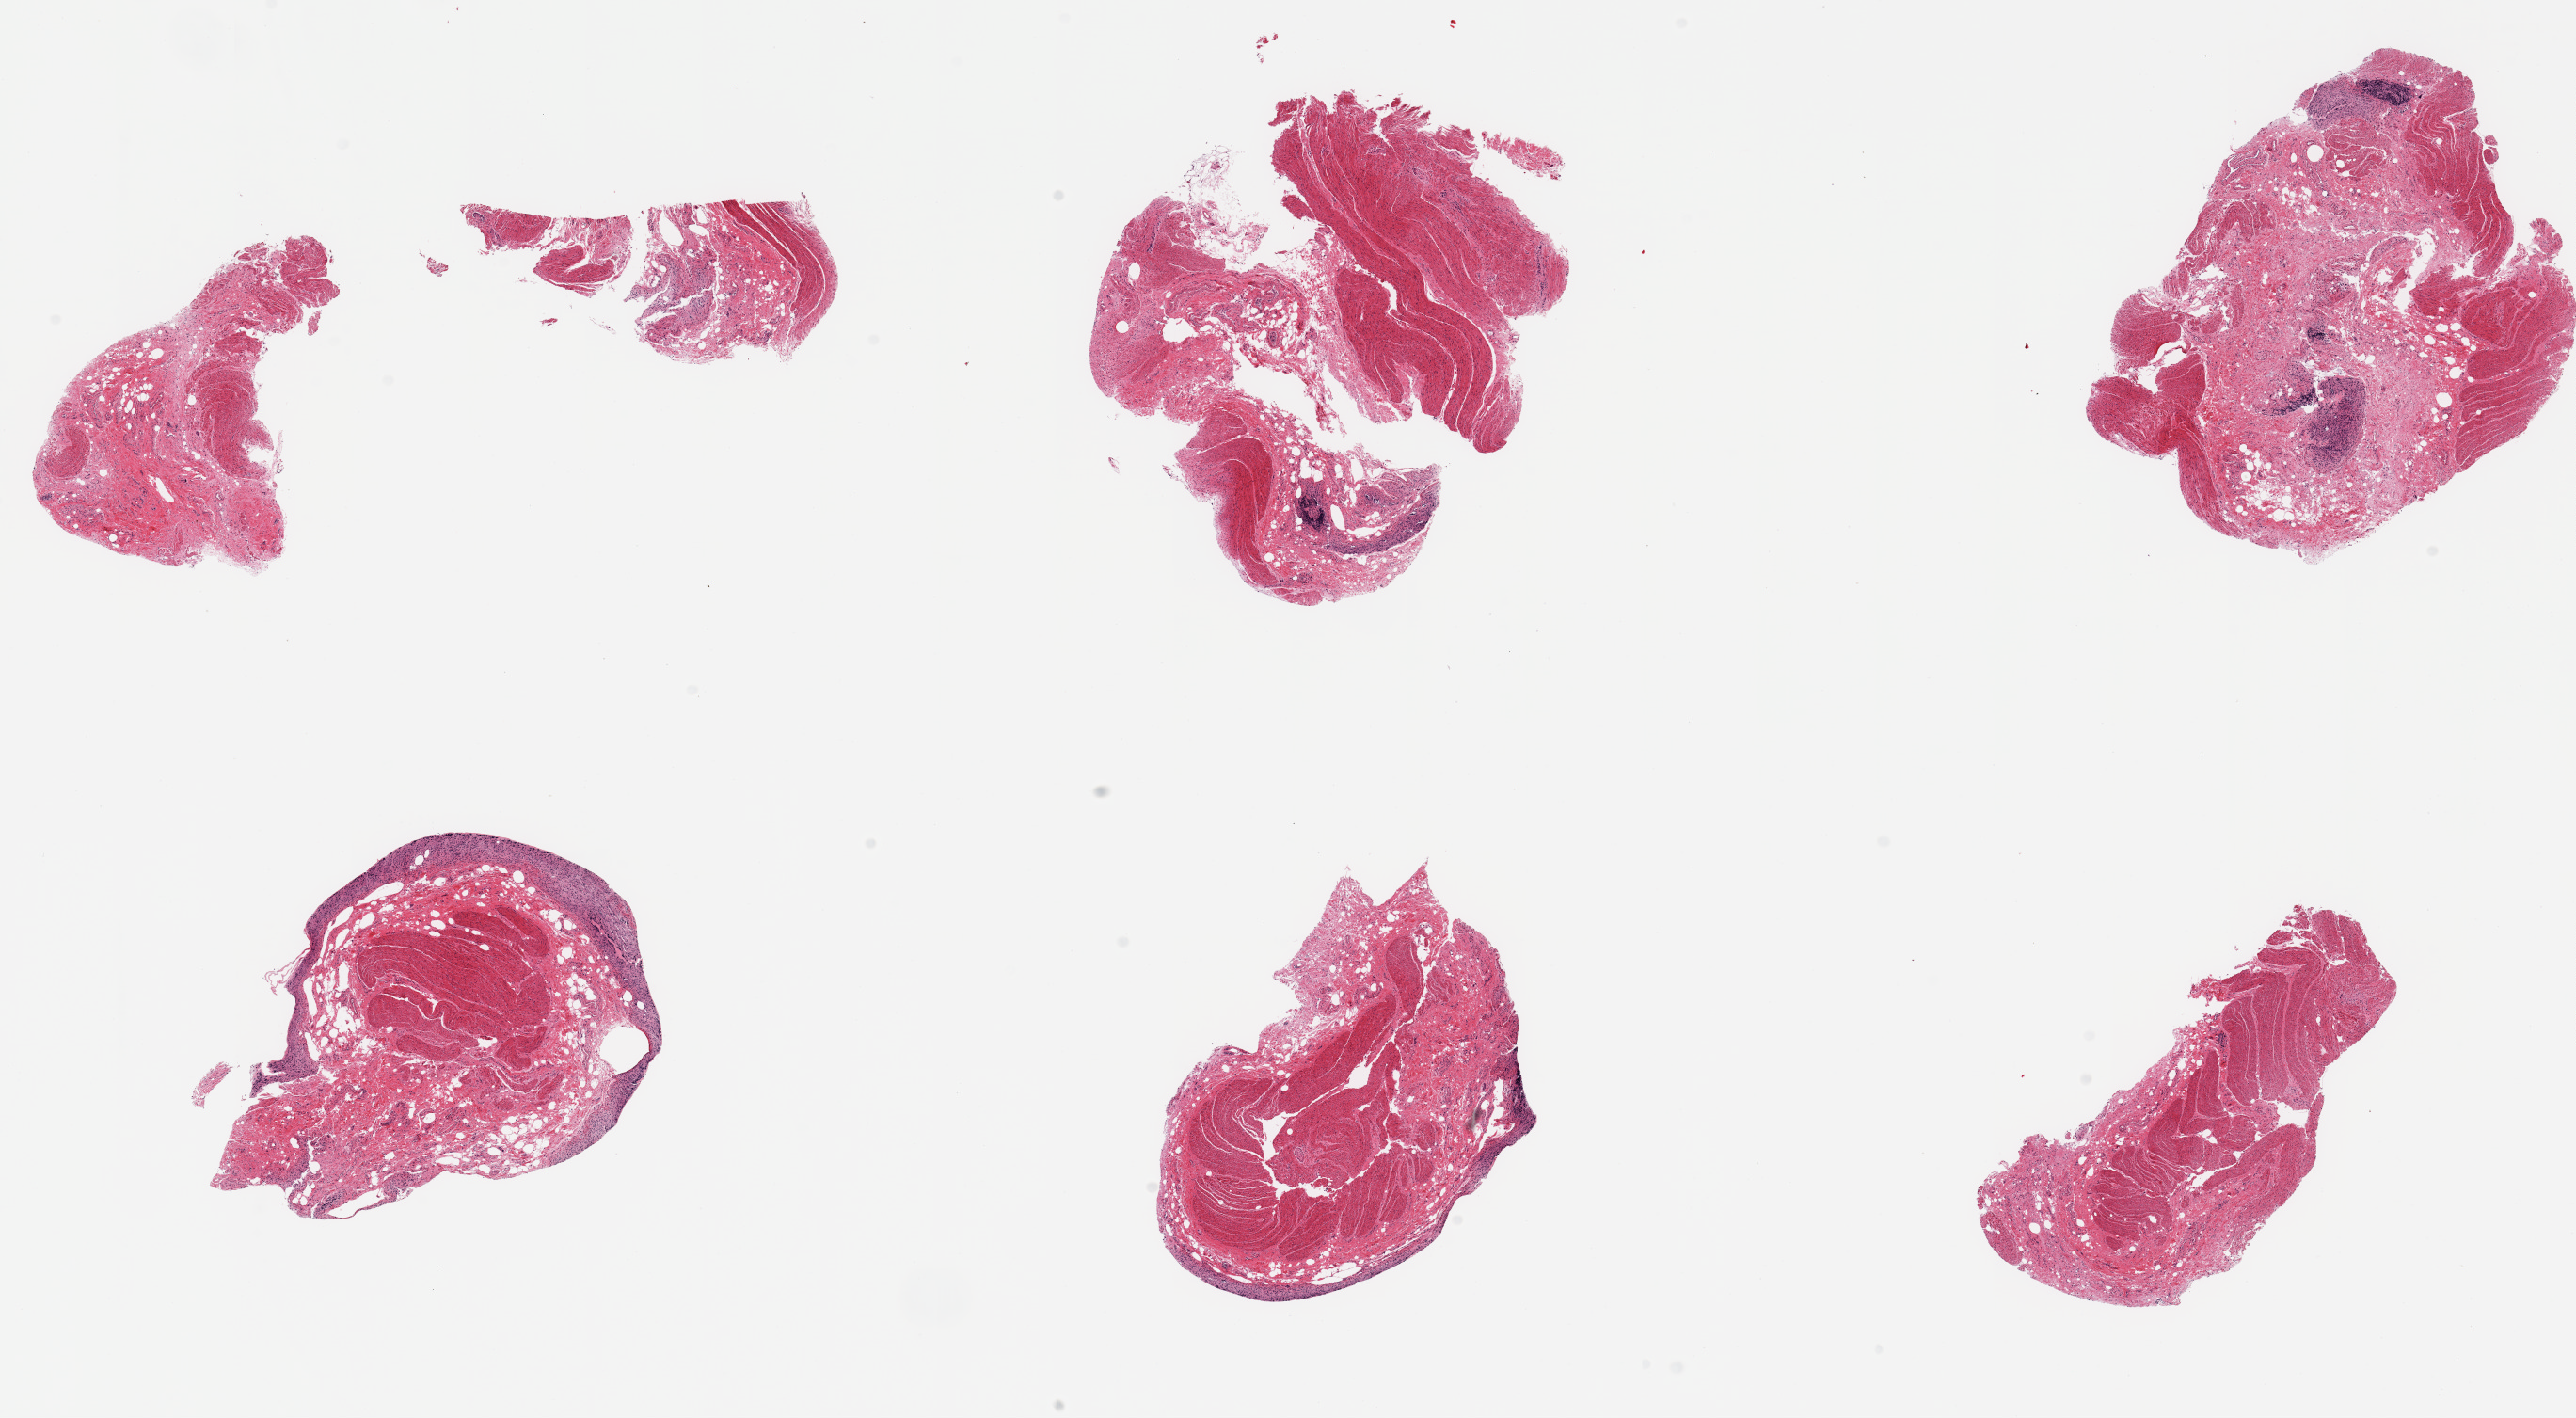
Hematoxylin and eosin (H&E) whole-slide image — a low-resolution overview of the entire scanned area, about 21.7 x 11.9 mm. PAXgene-fixed paraffin-embedded (PFPE) section. Target tissue: sigmoid colon. Donor tissue sample.
Review note (as recorded): 6 pieces, target muscularis, ~10% 'contaminant mucosa'.